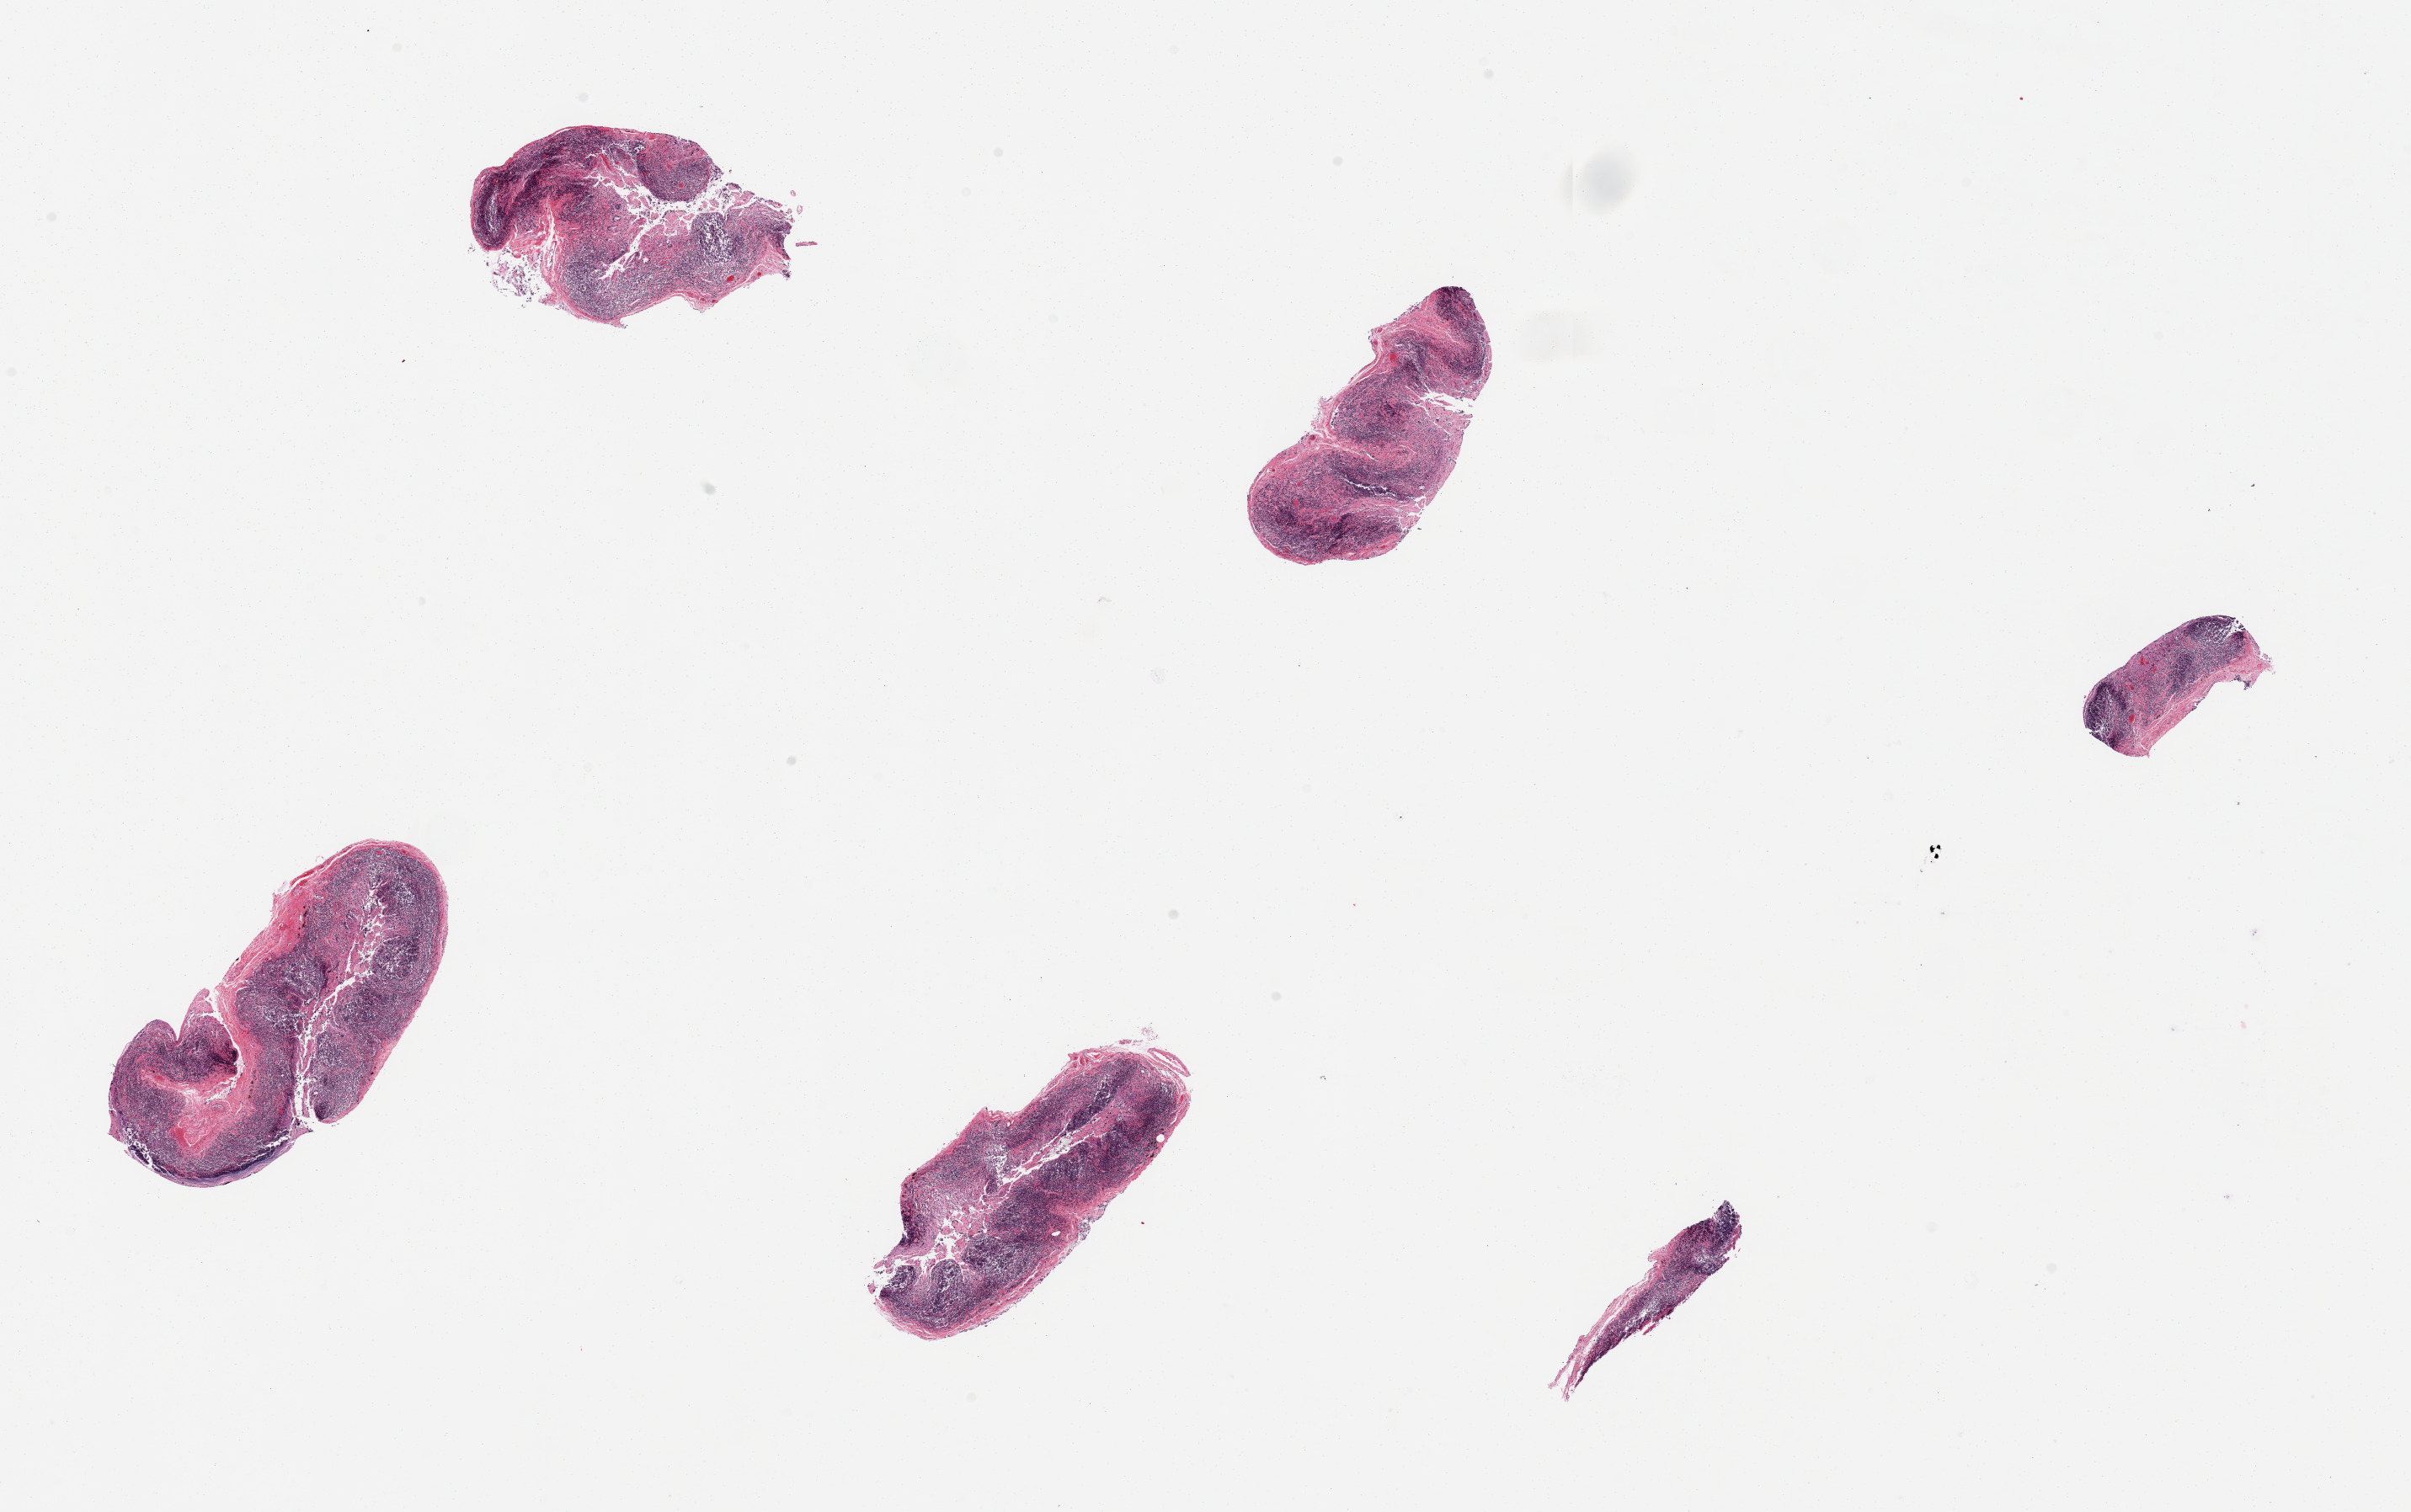
Whole-slide image, haematoxylin and eosin stain, a low-resolution overview of the entire scanned area, about 22.6 x 14.2 mm, PAXgene-fixed paraffin-embedded (PFPE) section, sampled site (target tissue): ileum, donor tissue sample. Female donor.
Reviewer comment on this tissue sample: 6 pieces, autolyzed mucosa with residual lymphoid component, well trimmed of muscularis.